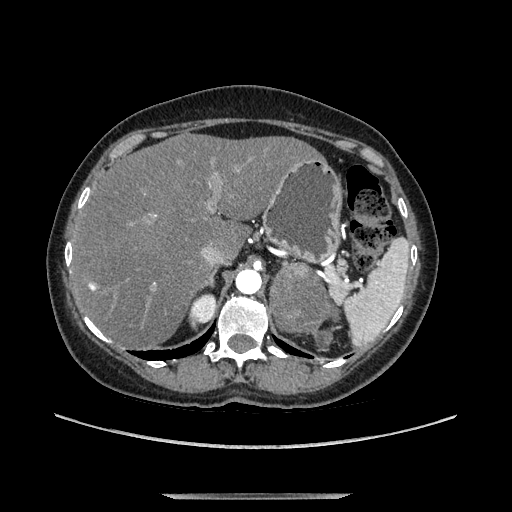
Contrast-enhanced abdominal CT, one axial slice. Slice 93 of 169 in the series (ordered by position). Soft-tissue window (W 400 / L 40 HU). 1.25 mm slice thickness. 512 × 512 image matrix. Female patient. From the clinical record (not read from this slice): diagnosis: adrenocortical carcinoma; tumour side: left adrenal; tumour size at pathology: 9 cm; Ki-67 index: 2 %; stage (as recorded): 3.
Annotated regions visible in this slice (semi-automatic segmentation, software-assisted and operator-edited):
- mass: bounding box [x1, y1, x2, y2] px = [272, 264, 331, 329]